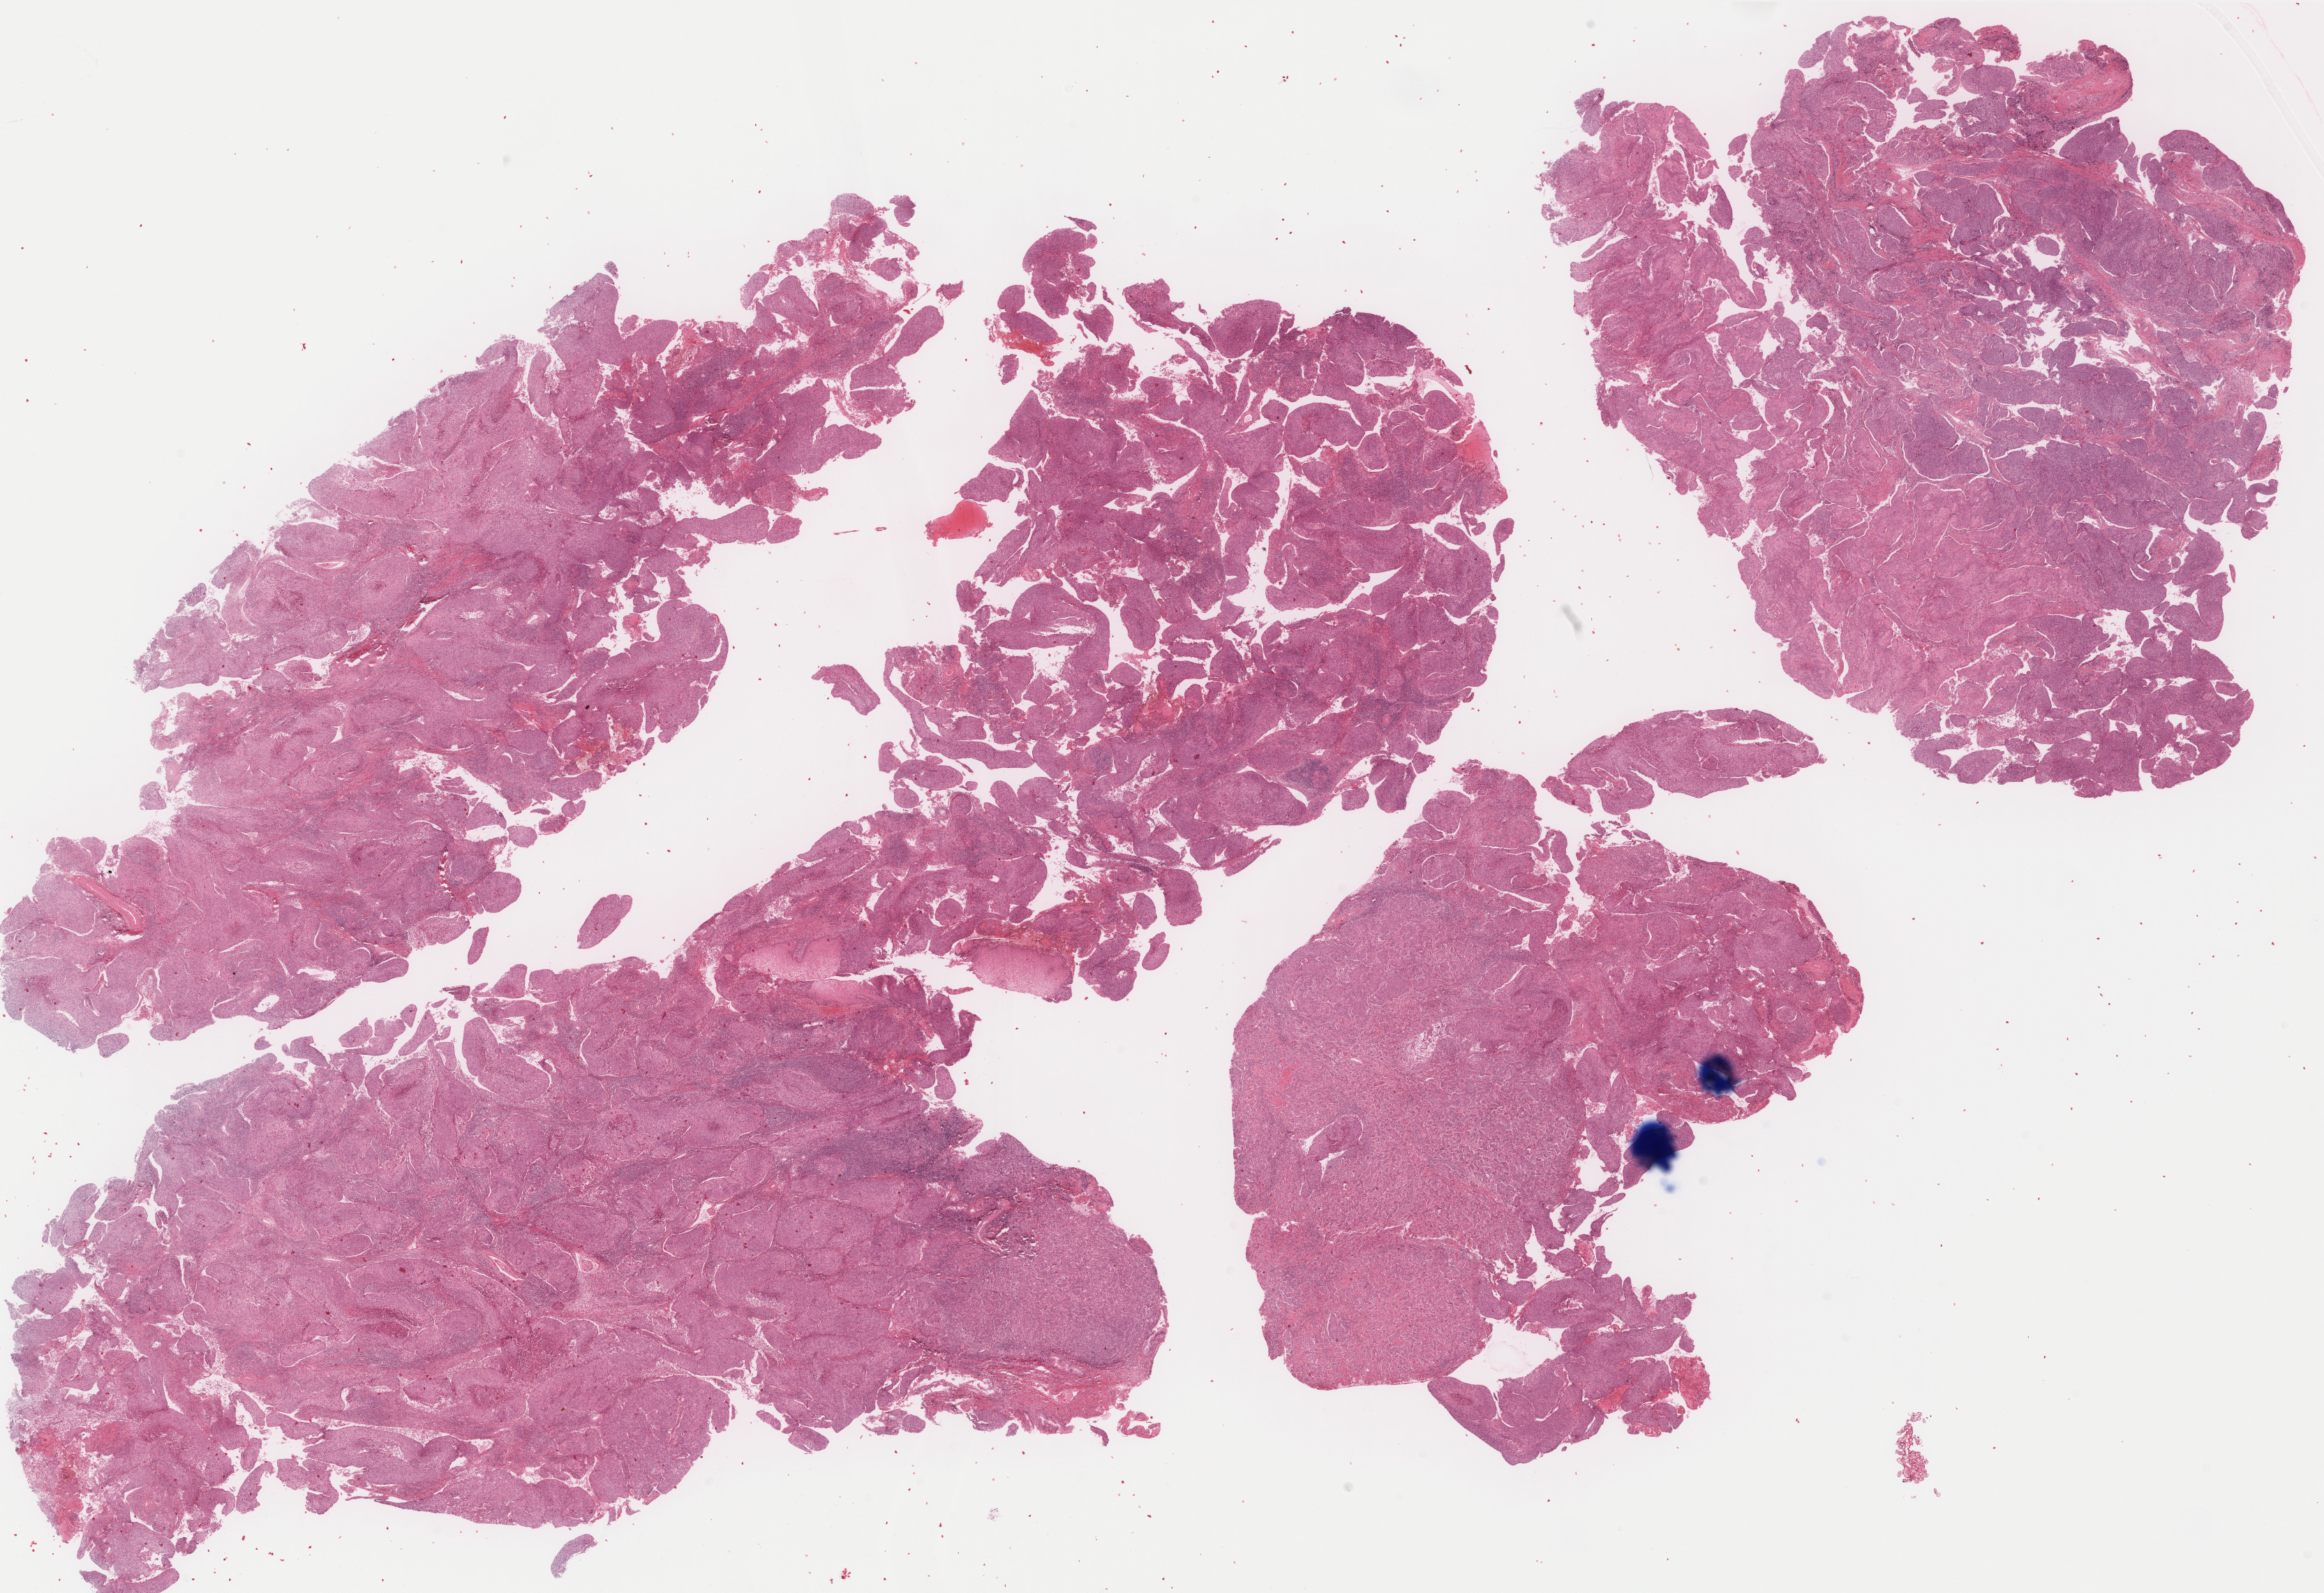
Digitized Hematoxylin and eosin (H&E) stained tissue section (whole slide) — a low-resolution overview of the entire scanned area, about 26.7 x 18.3 mm. Formalin-fixed paraffin-embedded (FFPE) diagnostic section. Cervix, primary tumour sample. Female patient; age at initial diagnosis 31 years. Histologic grade: G2 (moderately differentiated).
* diagnosis: Squamous cell carcinoma, NOS
* FIGO stage: IIIB